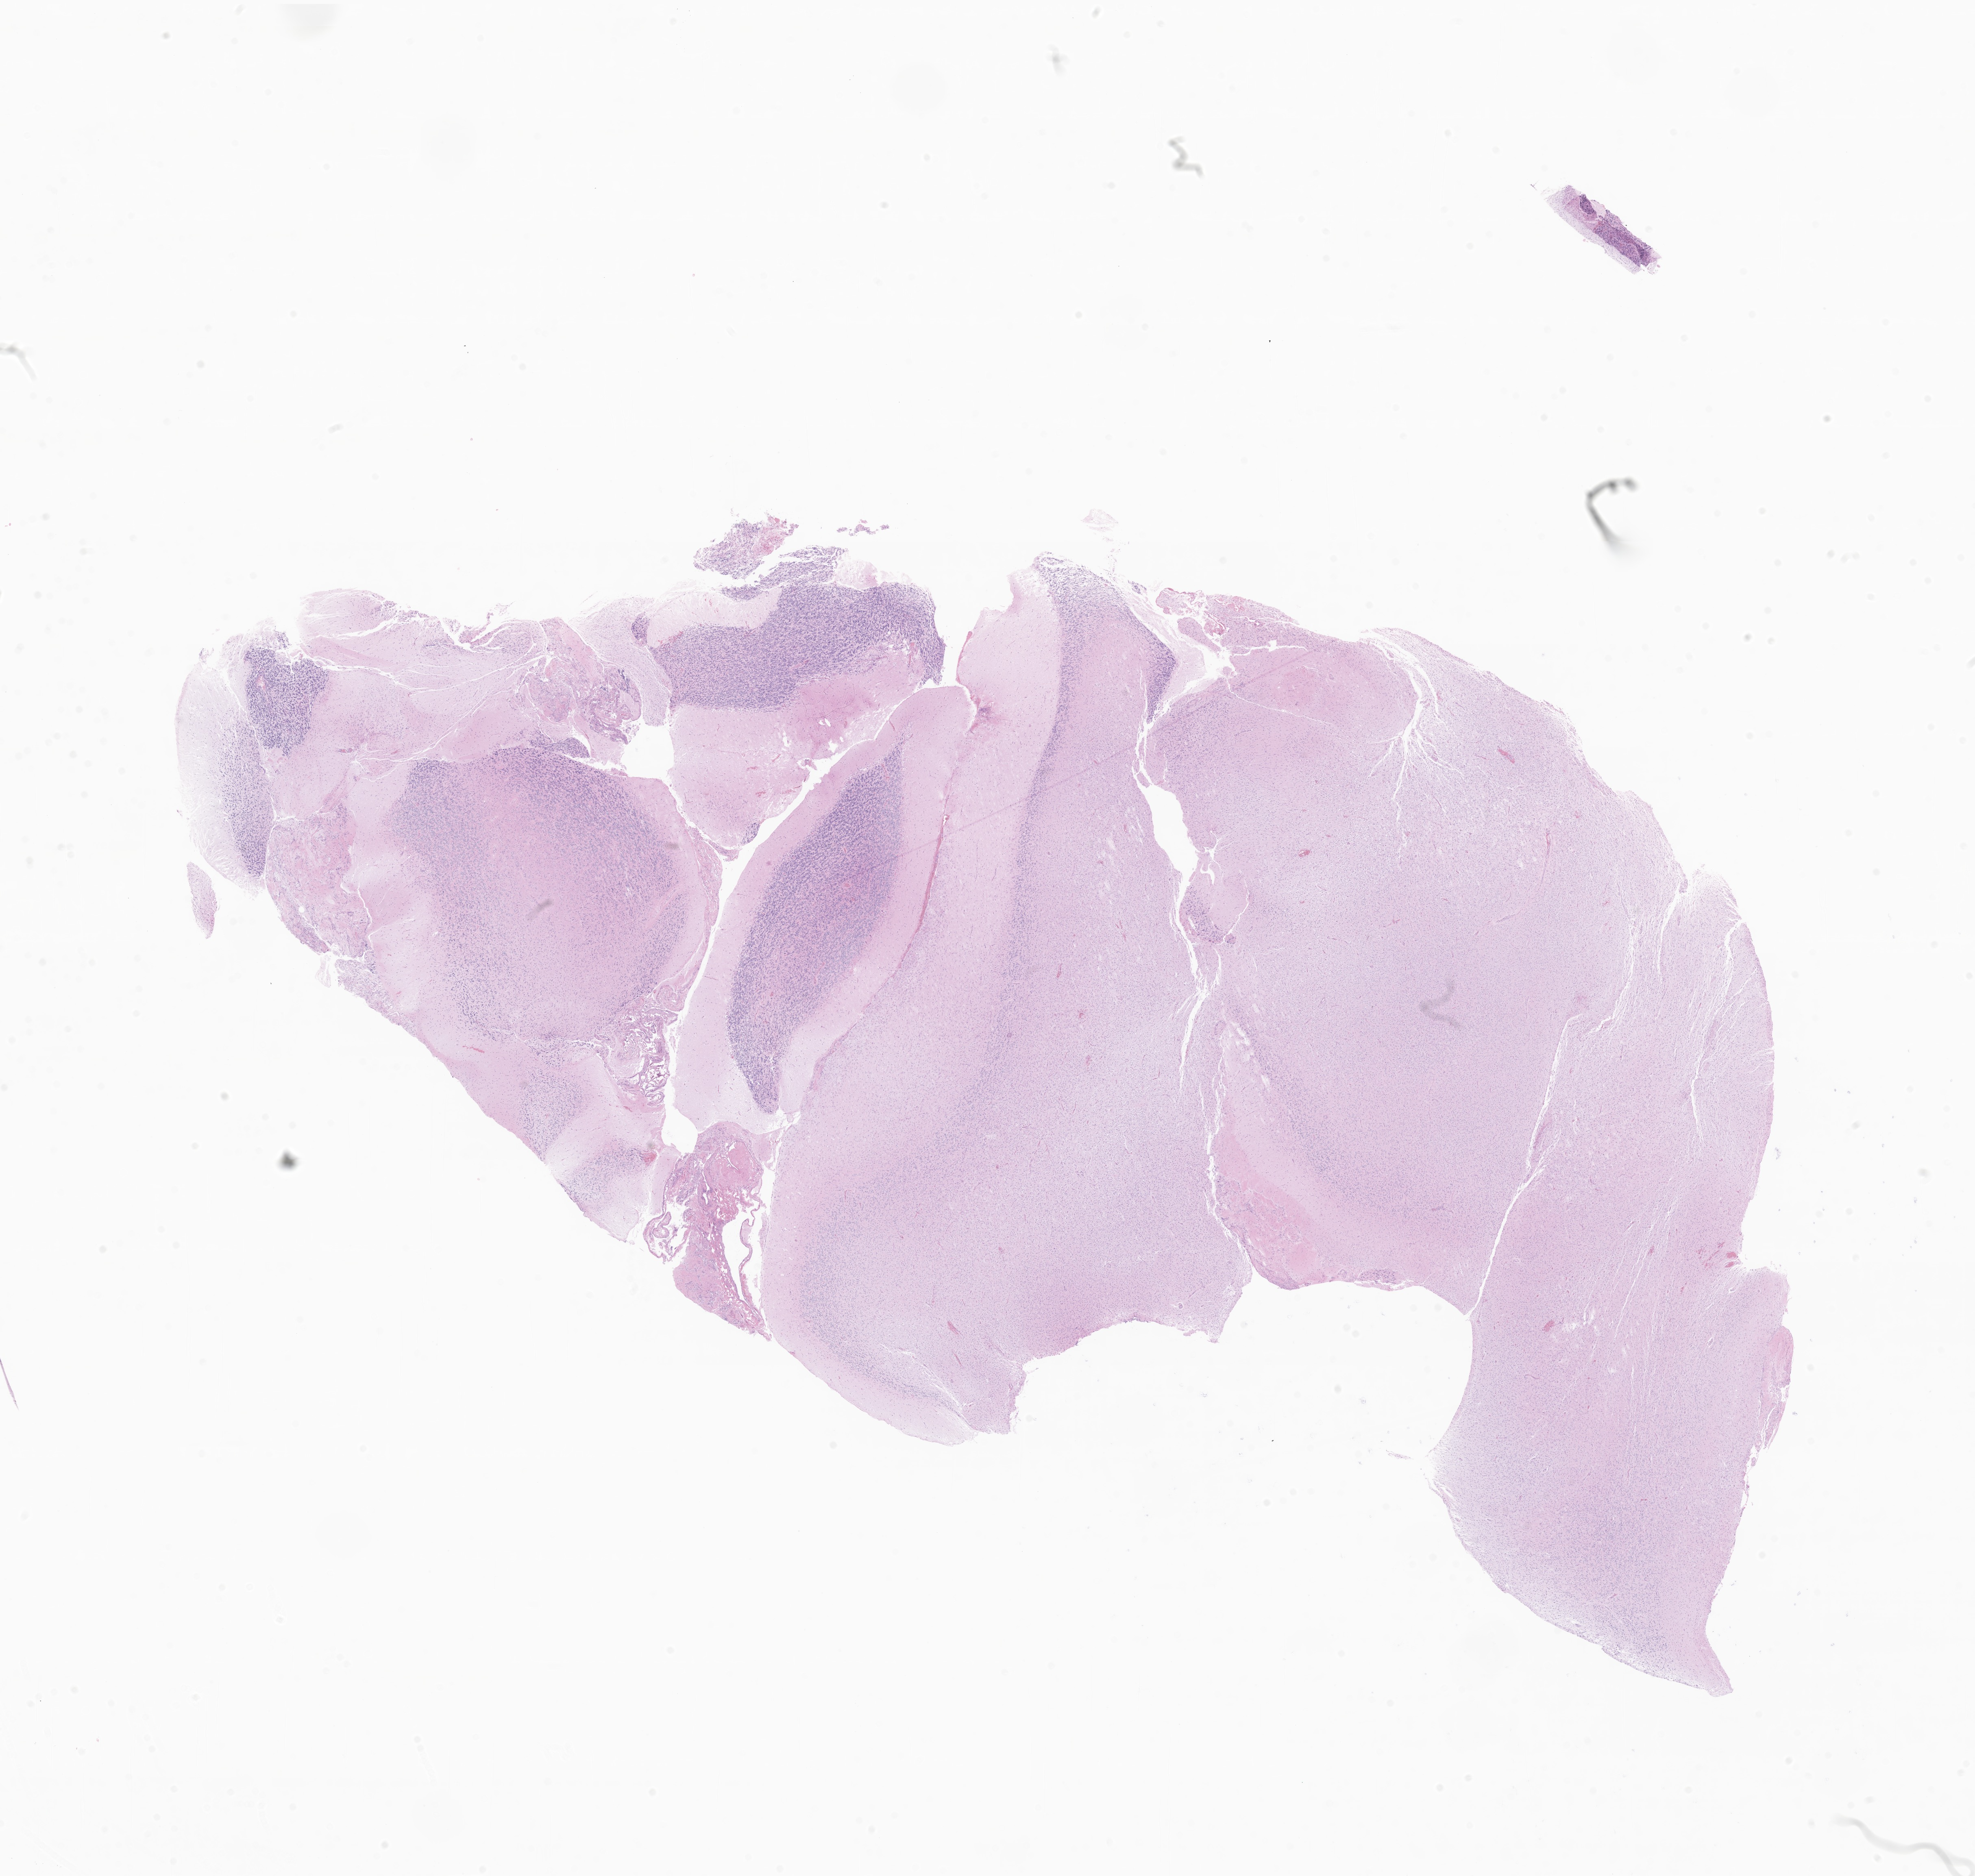
Digitized hematoxylin and eosin (H&E)-stained section of tumor tissue from the cerebellum, whole scanned area (about 20.5 x 19.4 mm) shown as a low-resolution overview; formalin-fixed paraffin-embedded section. Male patient, age 100 months (8 years 4 months).
Diagnosis (ICD-O-3 morphology term): Pilocytic astrocytoma.